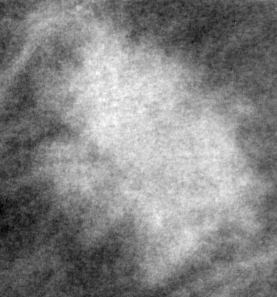
Cropped region of a digitized screen-film mammogram centred on a radiologist-marked abnormality, left breast, MLO view, BI-RADS breast density category 3 (scale 1–4).
- Mass, shape irregular, margins spiculated; BI-RADS assessment category 5; subtlety rating 4 on a 1 (subtle) to 5 (obvious) scale; pathology (as recorded): malignant.